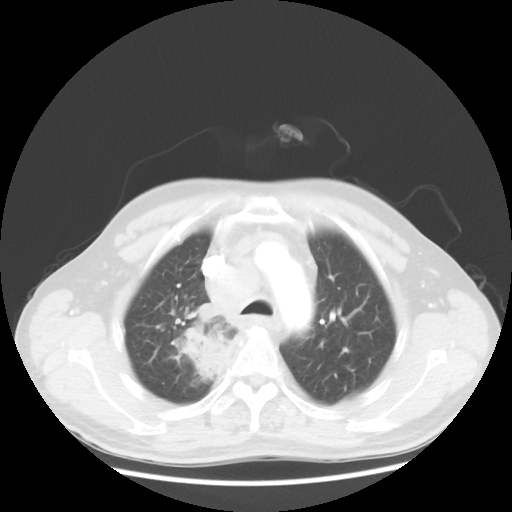
Chest CT, one axial slice; slice 95 of 124 in the series (ordered by position); reconstruction kernel STANDARD; 100 kVp; lung window (W 1500 / L -600 HU); 5 mm slice thickness; 512 × 512 image matrix, field of view 382 × 382 mm. Male patient, age 64 years. Case-level facts recorded for this patient, not image findings: clinical TNM (as recorded): T3 N3 M0; histopathological grade: G3.
Structures marked on this image (bounding box drawn by a radiologist):
- lung tumour (recorded histology: small cell carcinoma): bounding box (x1, y1, x2, y2) in pixels: (173, 297, 240, 399)